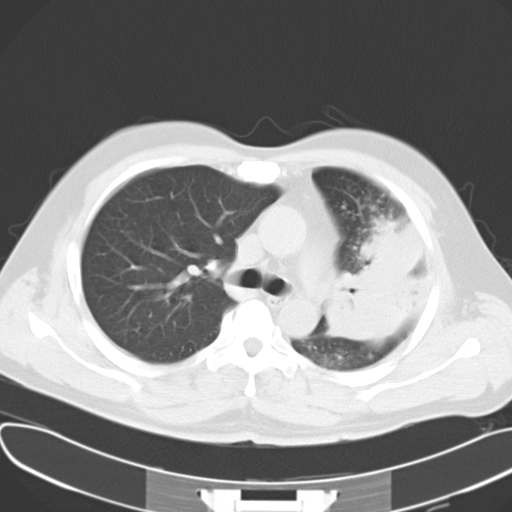
Chest CT, one axial slice. Reconstruction kernel B40f. 120 kVp. Lung window (W 1500 / L -600 HU). 512 × 512 image matrix, field of view 377 × 377 mm. Male patient, age 48 years. From the clinical record (not read from this slice): clinical TNM (as recorded): T4 N0 M0.
Annotated regions visible in this slice (bounding box drawn by a radiologist):
- lung tumour (recorded histology: adenocarcinoma): bounding box [x1, y1, x2, y2] px = [328, 209, 410, 343]